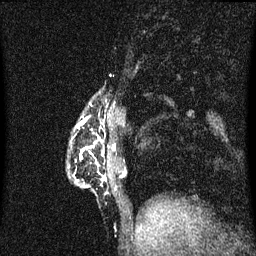
Breast MRI (dynamic contrast-enhanced), one sagittal slice; slice 12 of 60 in the series (ordered by position); dynamic contrast-enhanced series, image 2 of 3 at this slice position (ordered by acquisition); 1.5 T; TE 4.2 ms, TR 8.4 ms; 2 mm slice thickness; 256 × 256 image matrix, field of view 200 × 200 mm. Patient: female, 40 years.
Outlined on this slice (semi-automatically segmented with operator editing):
- analysis volume of interest (the breast-tissue region the enhancement analysis was run in; not a lesion): bounding box (x1, y1, x2, y2) in pixels: (68, 104, 107, 195)
- tumour enhancement mask (voxels above the 70 % enhancement threshold inside the analysis volume of interest): (78, 122, 107, 181)